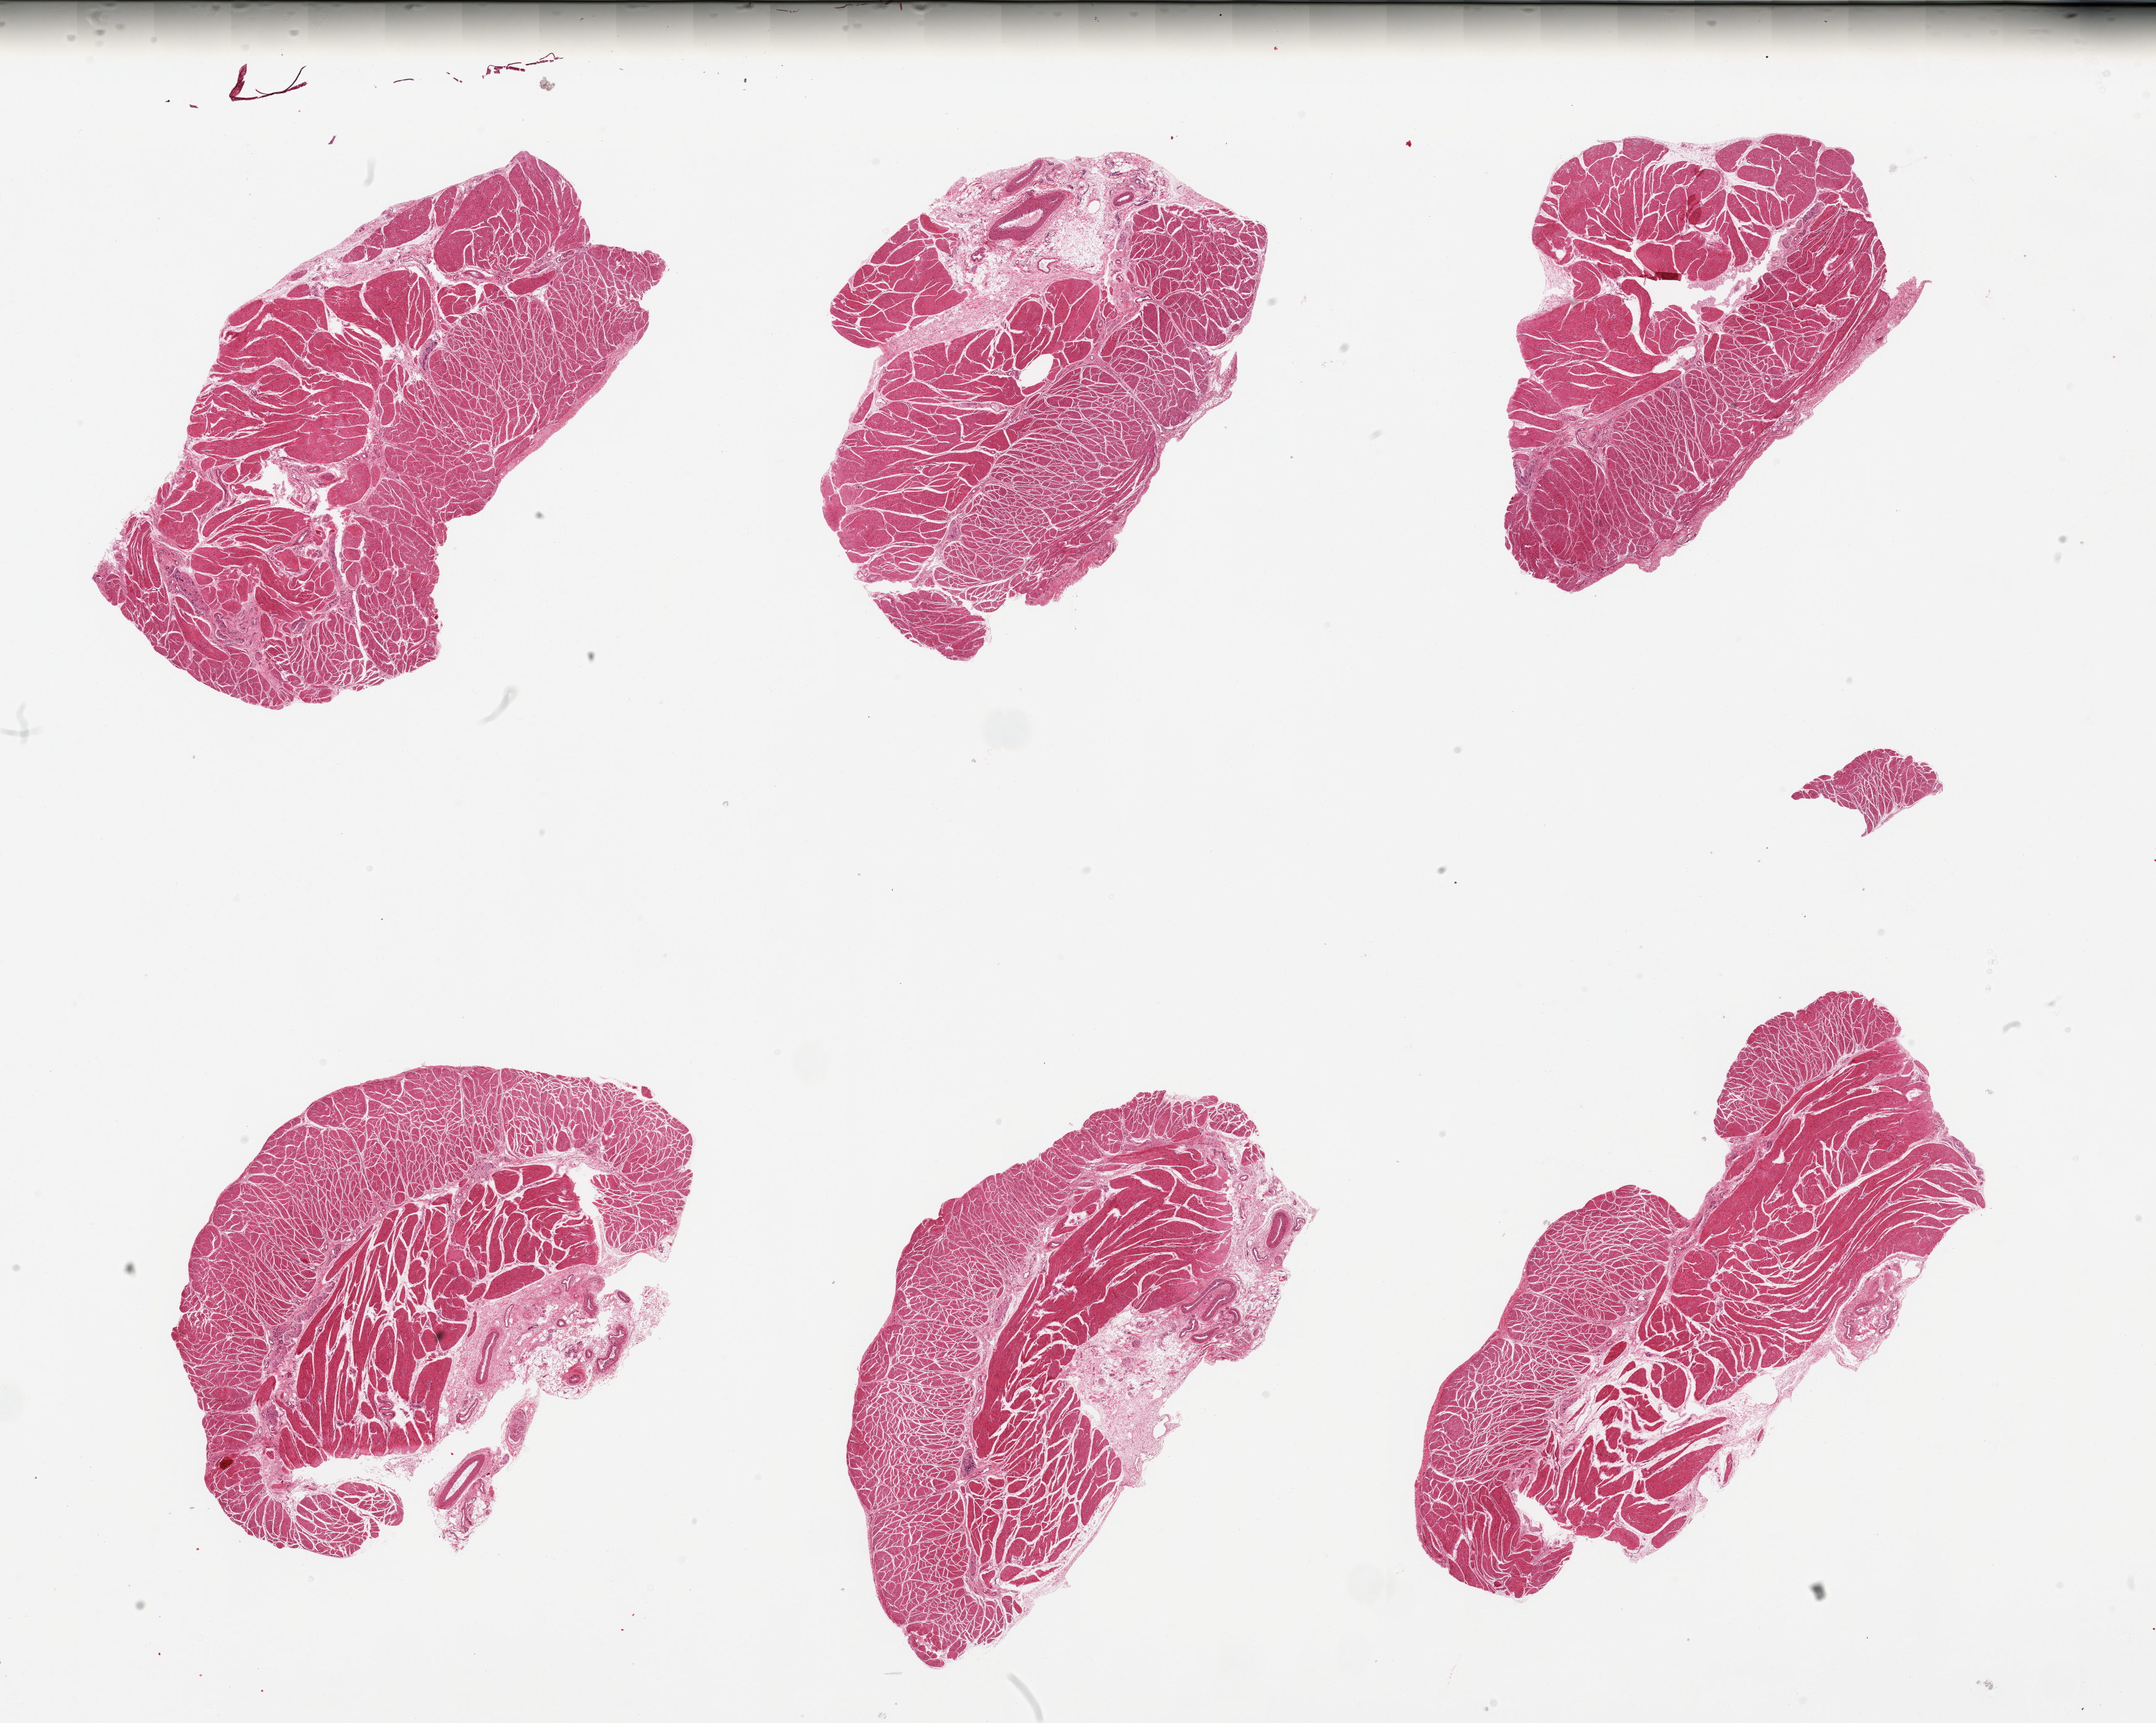
Whole-slide image, H&E stain, a low-resolution overview of the entire scanned area, about 27.6 x 22.0 mm. PAXgene-fixed, paraffin-embedded tissue. Target tissue: esophageal muscle. Tissue donor sample.
* pathologist's review note for this sample: 6 pieces; well trimmed